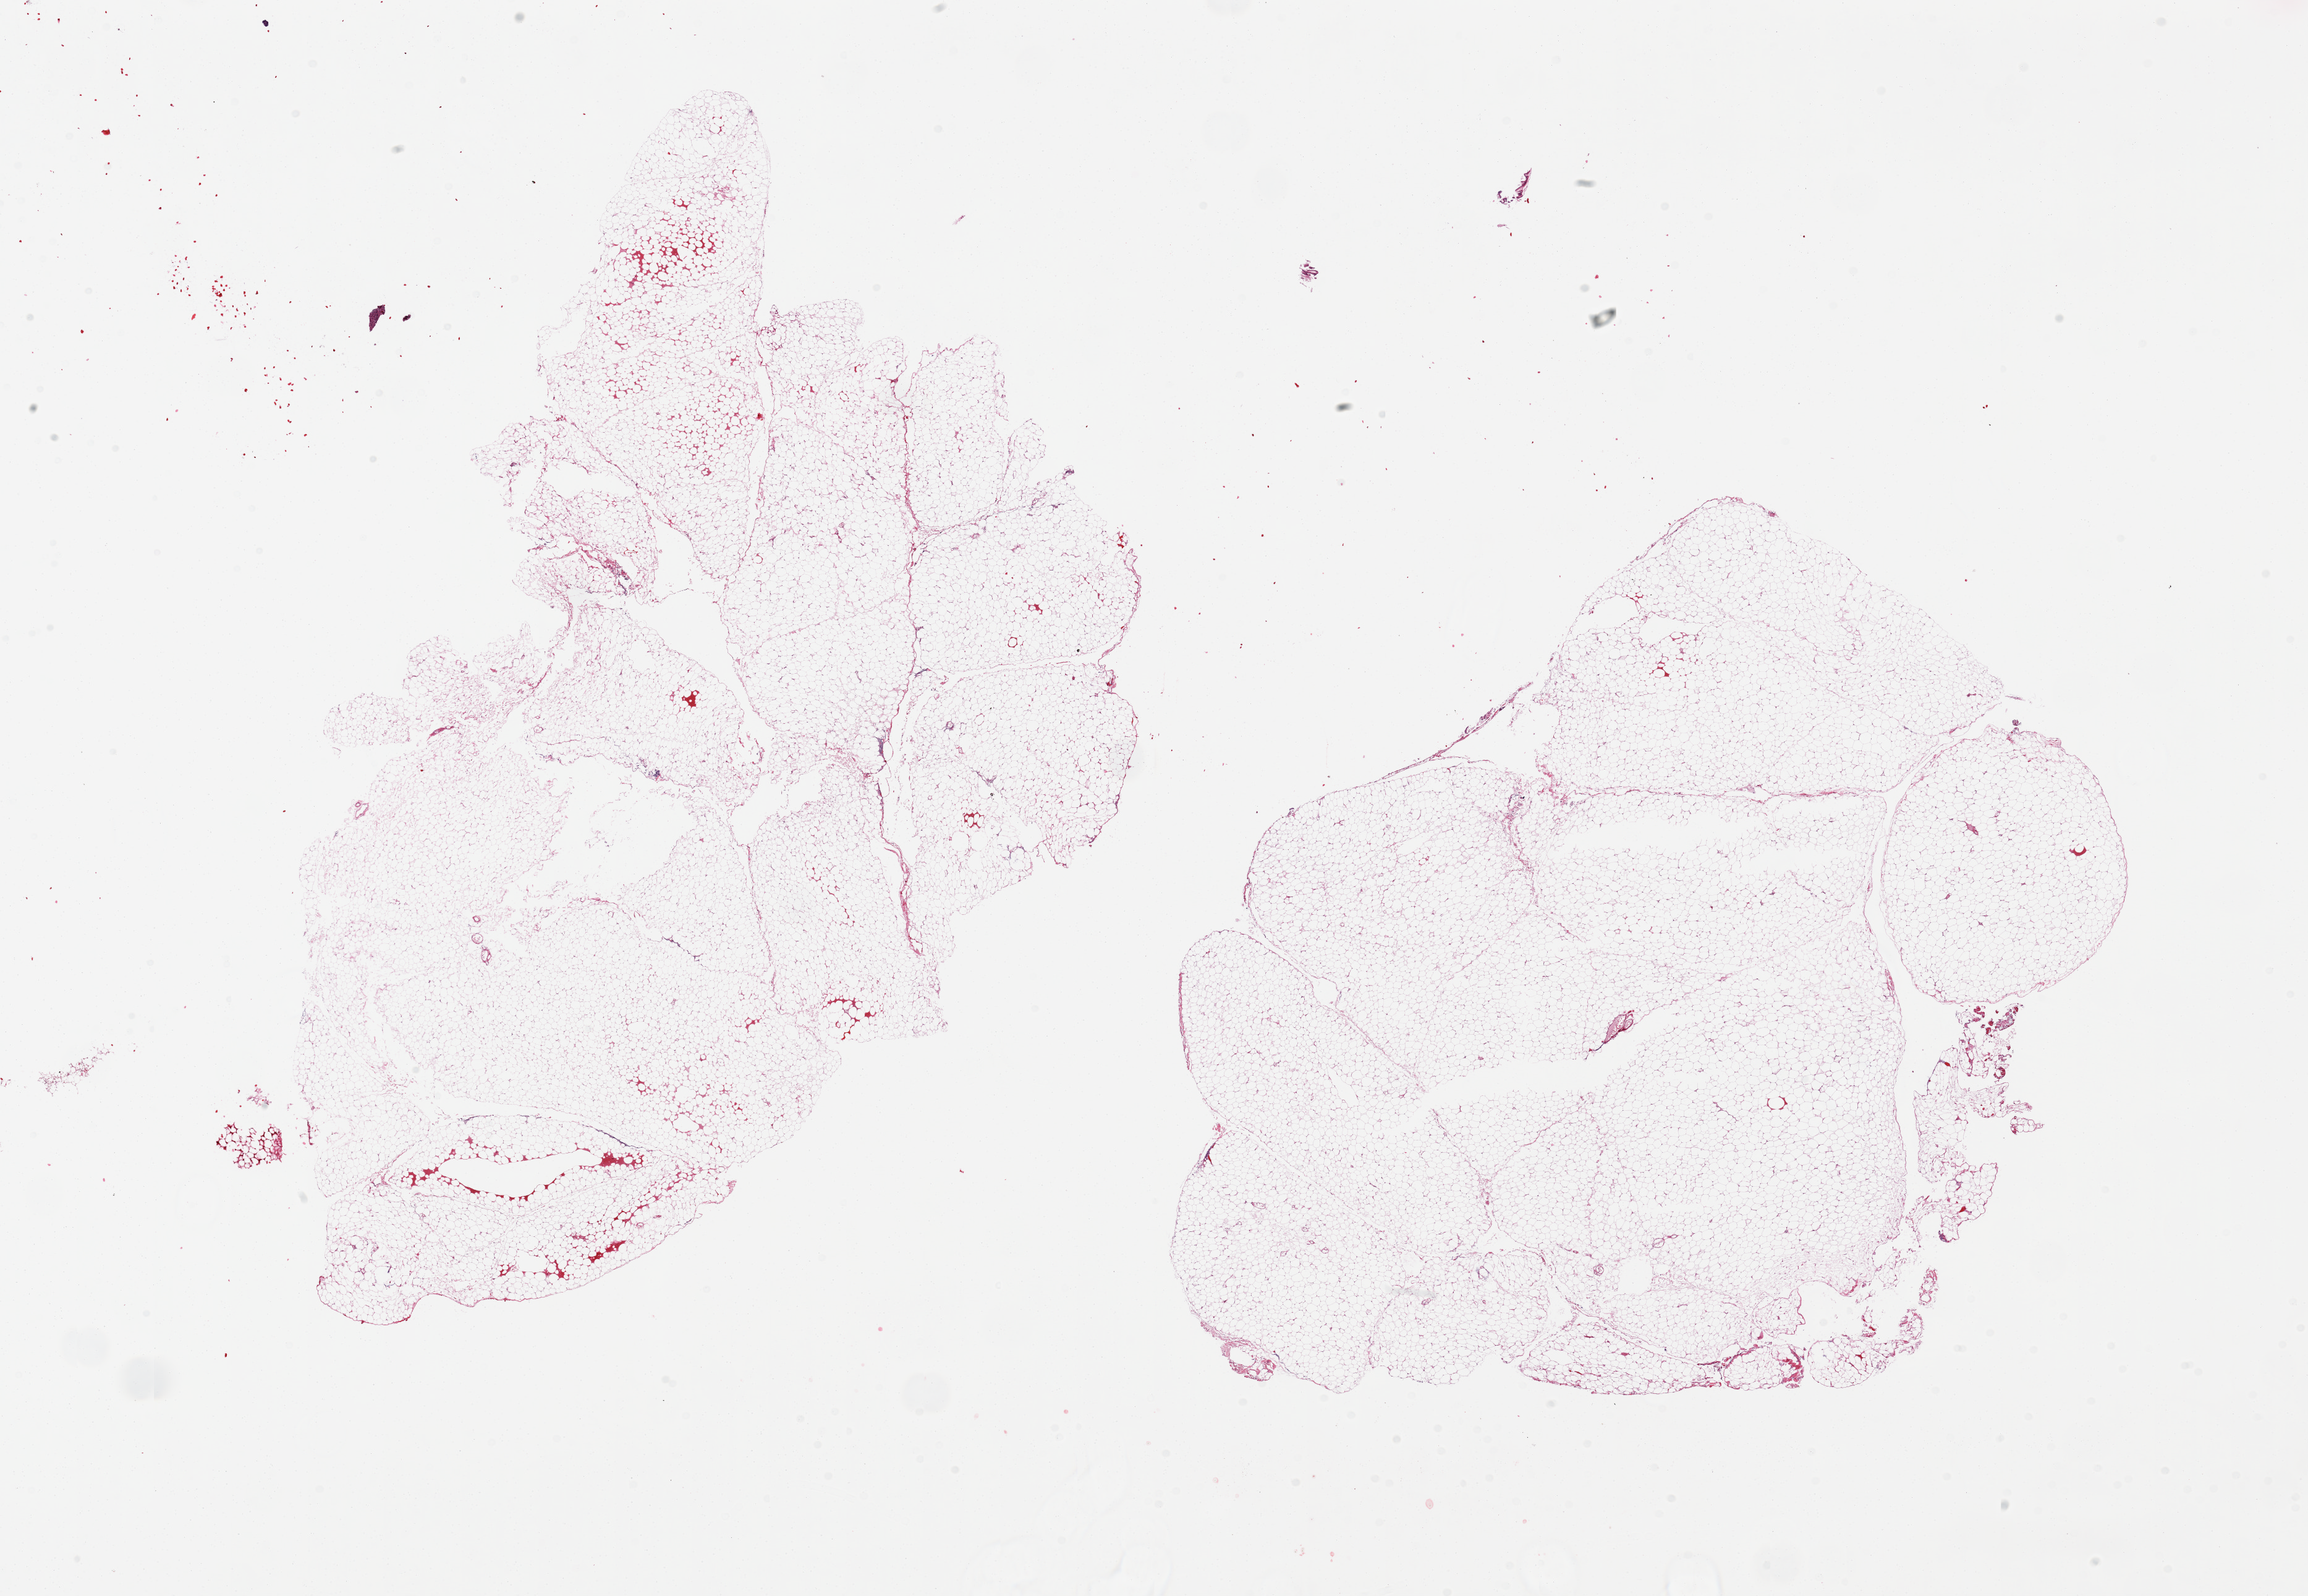
Whole-slide image, haematoxylin and eosin stain — low-resolution overview of the scanned area, about 29.5 x 20.4 mm (acquisition: 20x scan). PAXgene-fixed, paraffin-embedded tissue. Section of omentum (target tissue). Donor tissue sample. Donor sex: male.
- reviewer comment on this tissue sample: 2 pieces